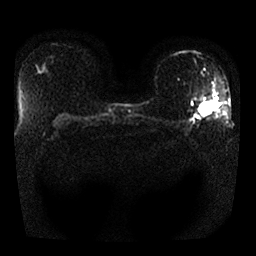
Breast MRI, one axial slice. Position 17 of 25 along the scan axis. Diffusion-weighted series; image 2 of 4 stored at this slice position (different b-values; order by instance number). 1.5 T. 256 × 256 image matrix. Female patient.
Outlined on this slice (expert manual segmentation):
- tumour on diffusion-weighted imaging: bounding box [x1, y1, x2, y2] px = [198, 103, 212, 116]